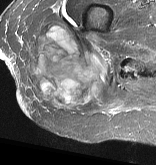
MRI of an extremity soft-tissue mass, one axial slice; slice 19 of 57 in the series (ordered by position); STIR; MR volume resampled by the dataset authors to the PET/CT grid (not the native acquisition matrix); 156 × 165 image matrix, field of view 152 × 161 mm. Female patient. From the clinical record (not read from this slice): histological type: epithelioid sarcoma with vascular differentiation; site of the primary tumour: right buttock.
Structures marked on this image (expert contour drawn on MRI and transferred to this co-registered scan by the dataset authors):
- gross tumour volume (mass): bounding box [x1, y1, x2, y2] px = [26, 21, 112, 111]